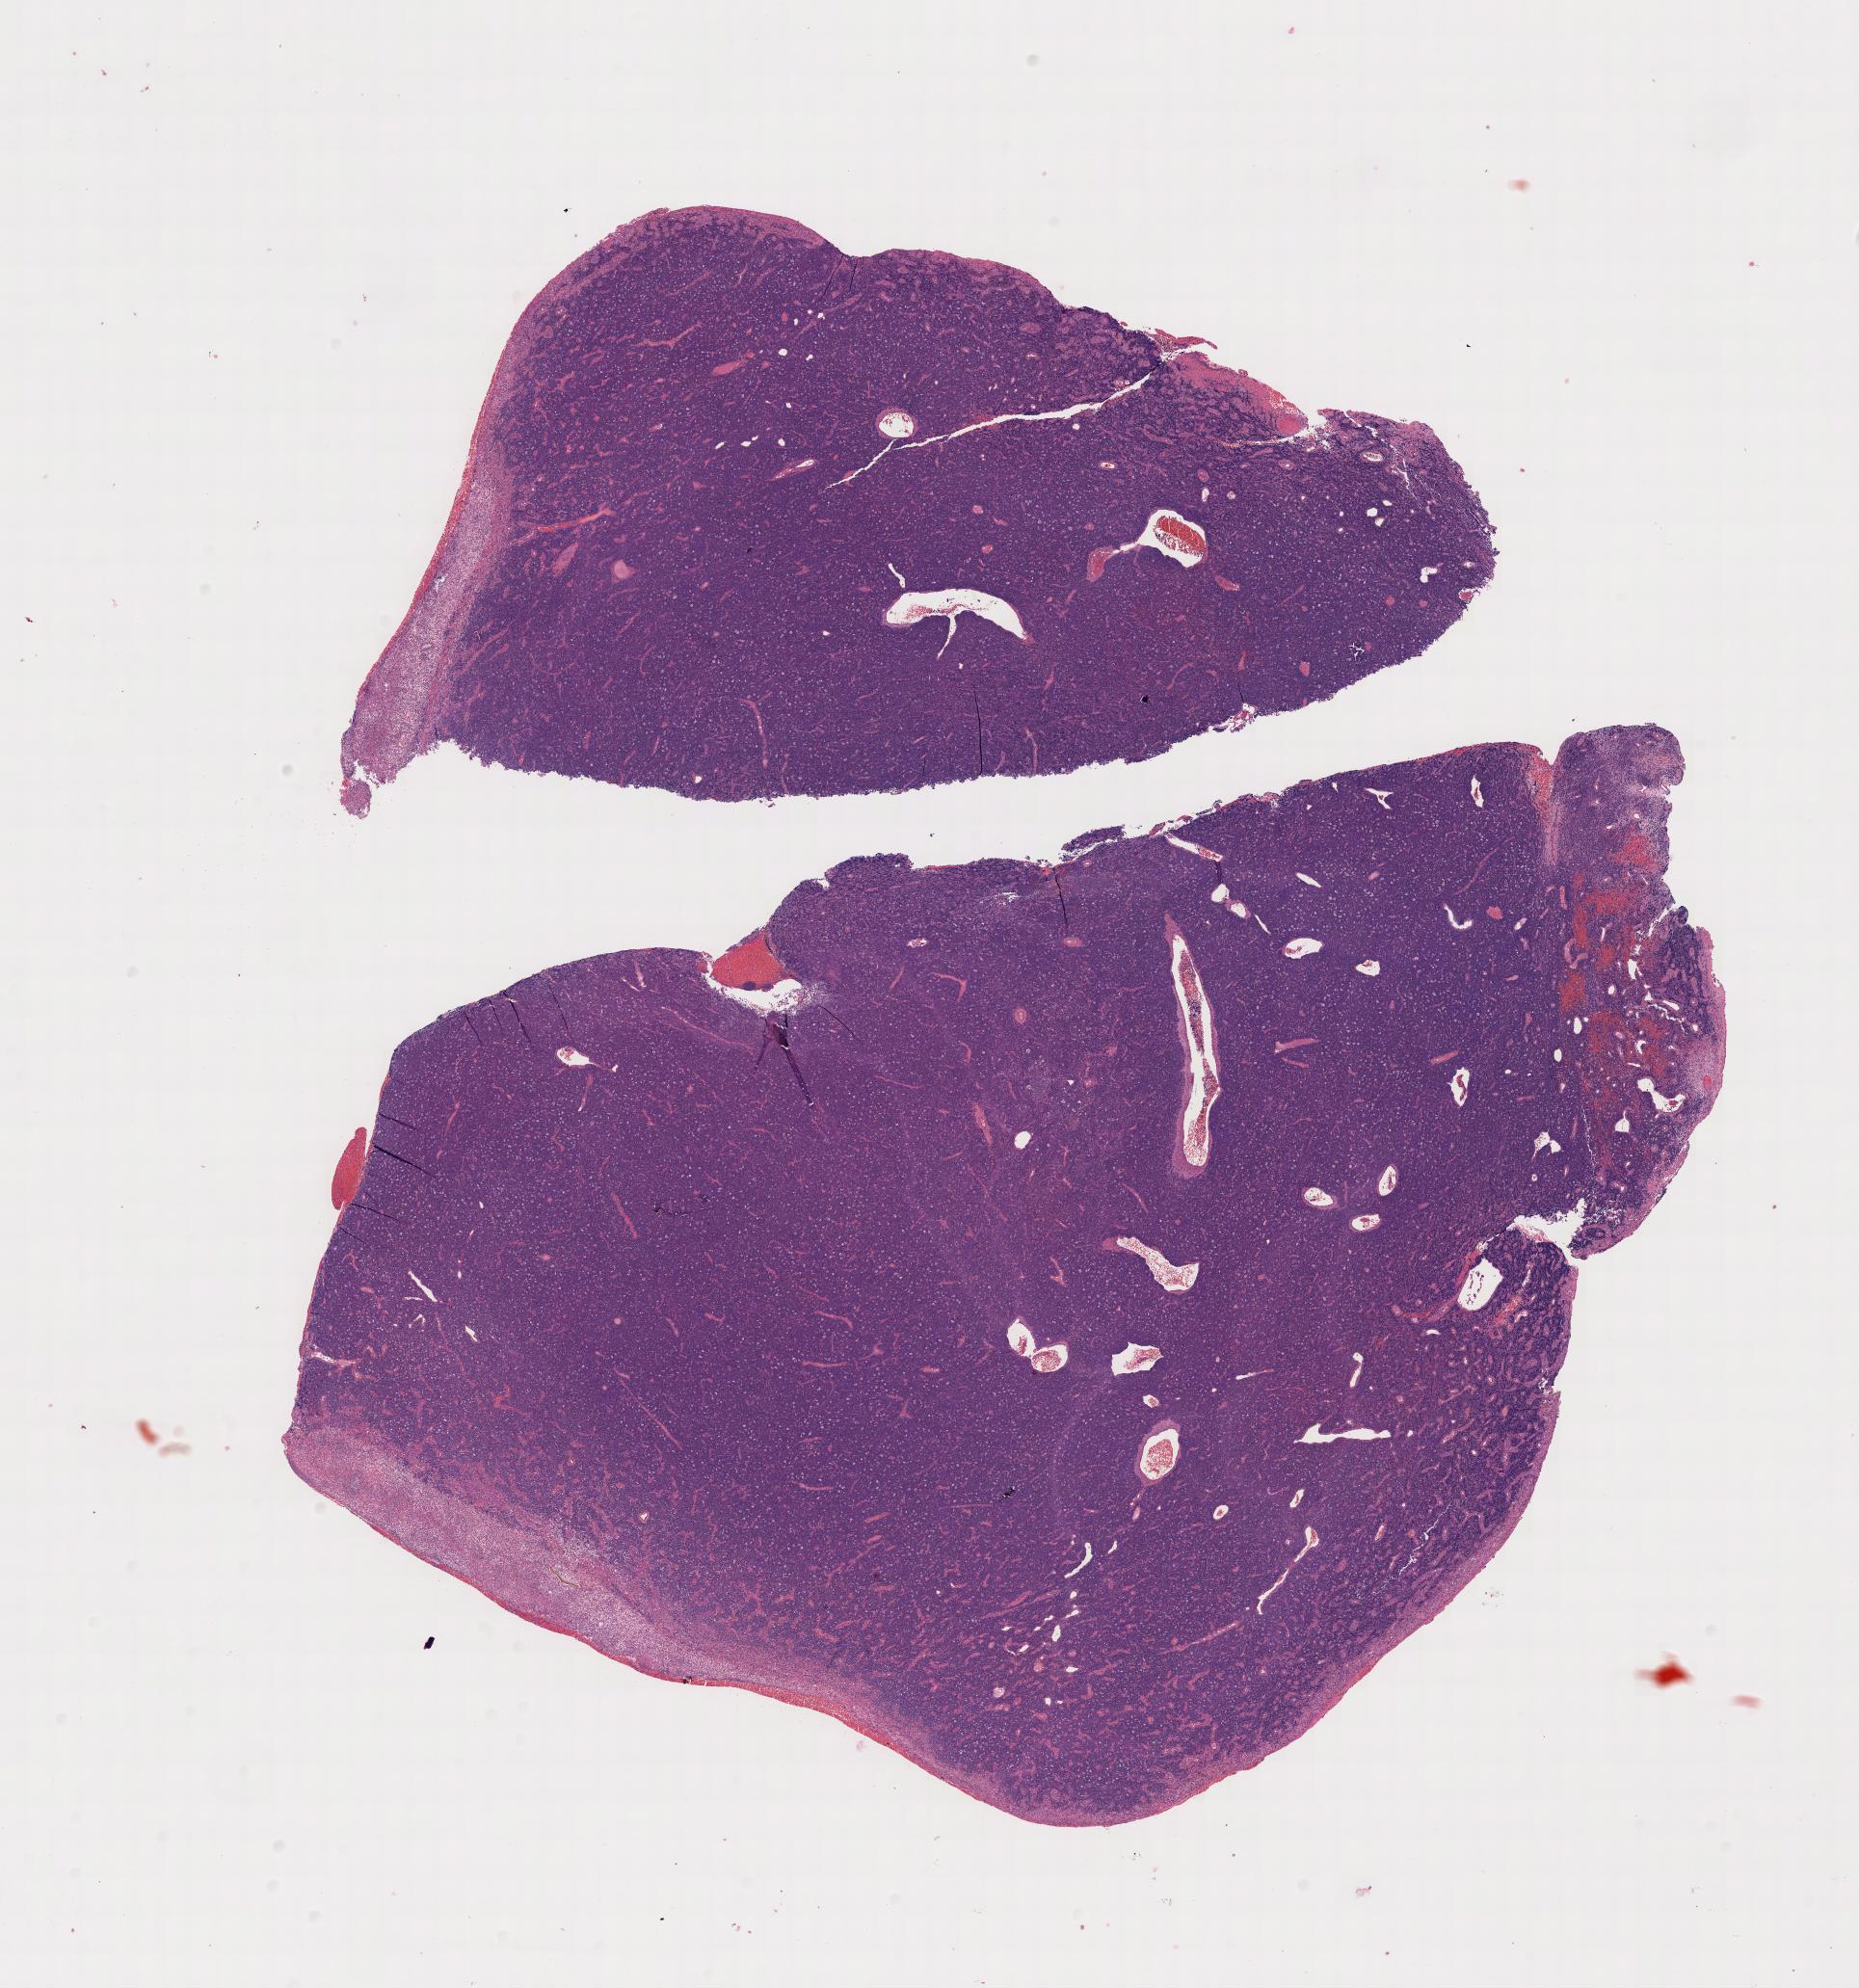
Digitized hematoxylin and eosin (H&E)-stained section — shown as a low-resolution overview of the whole scanned area, specimen: tumor tissue, site: cranium. Patient: female, age at initial diagnosis 6 years.
• diagnosis: Burkitt lymphoma, NOS